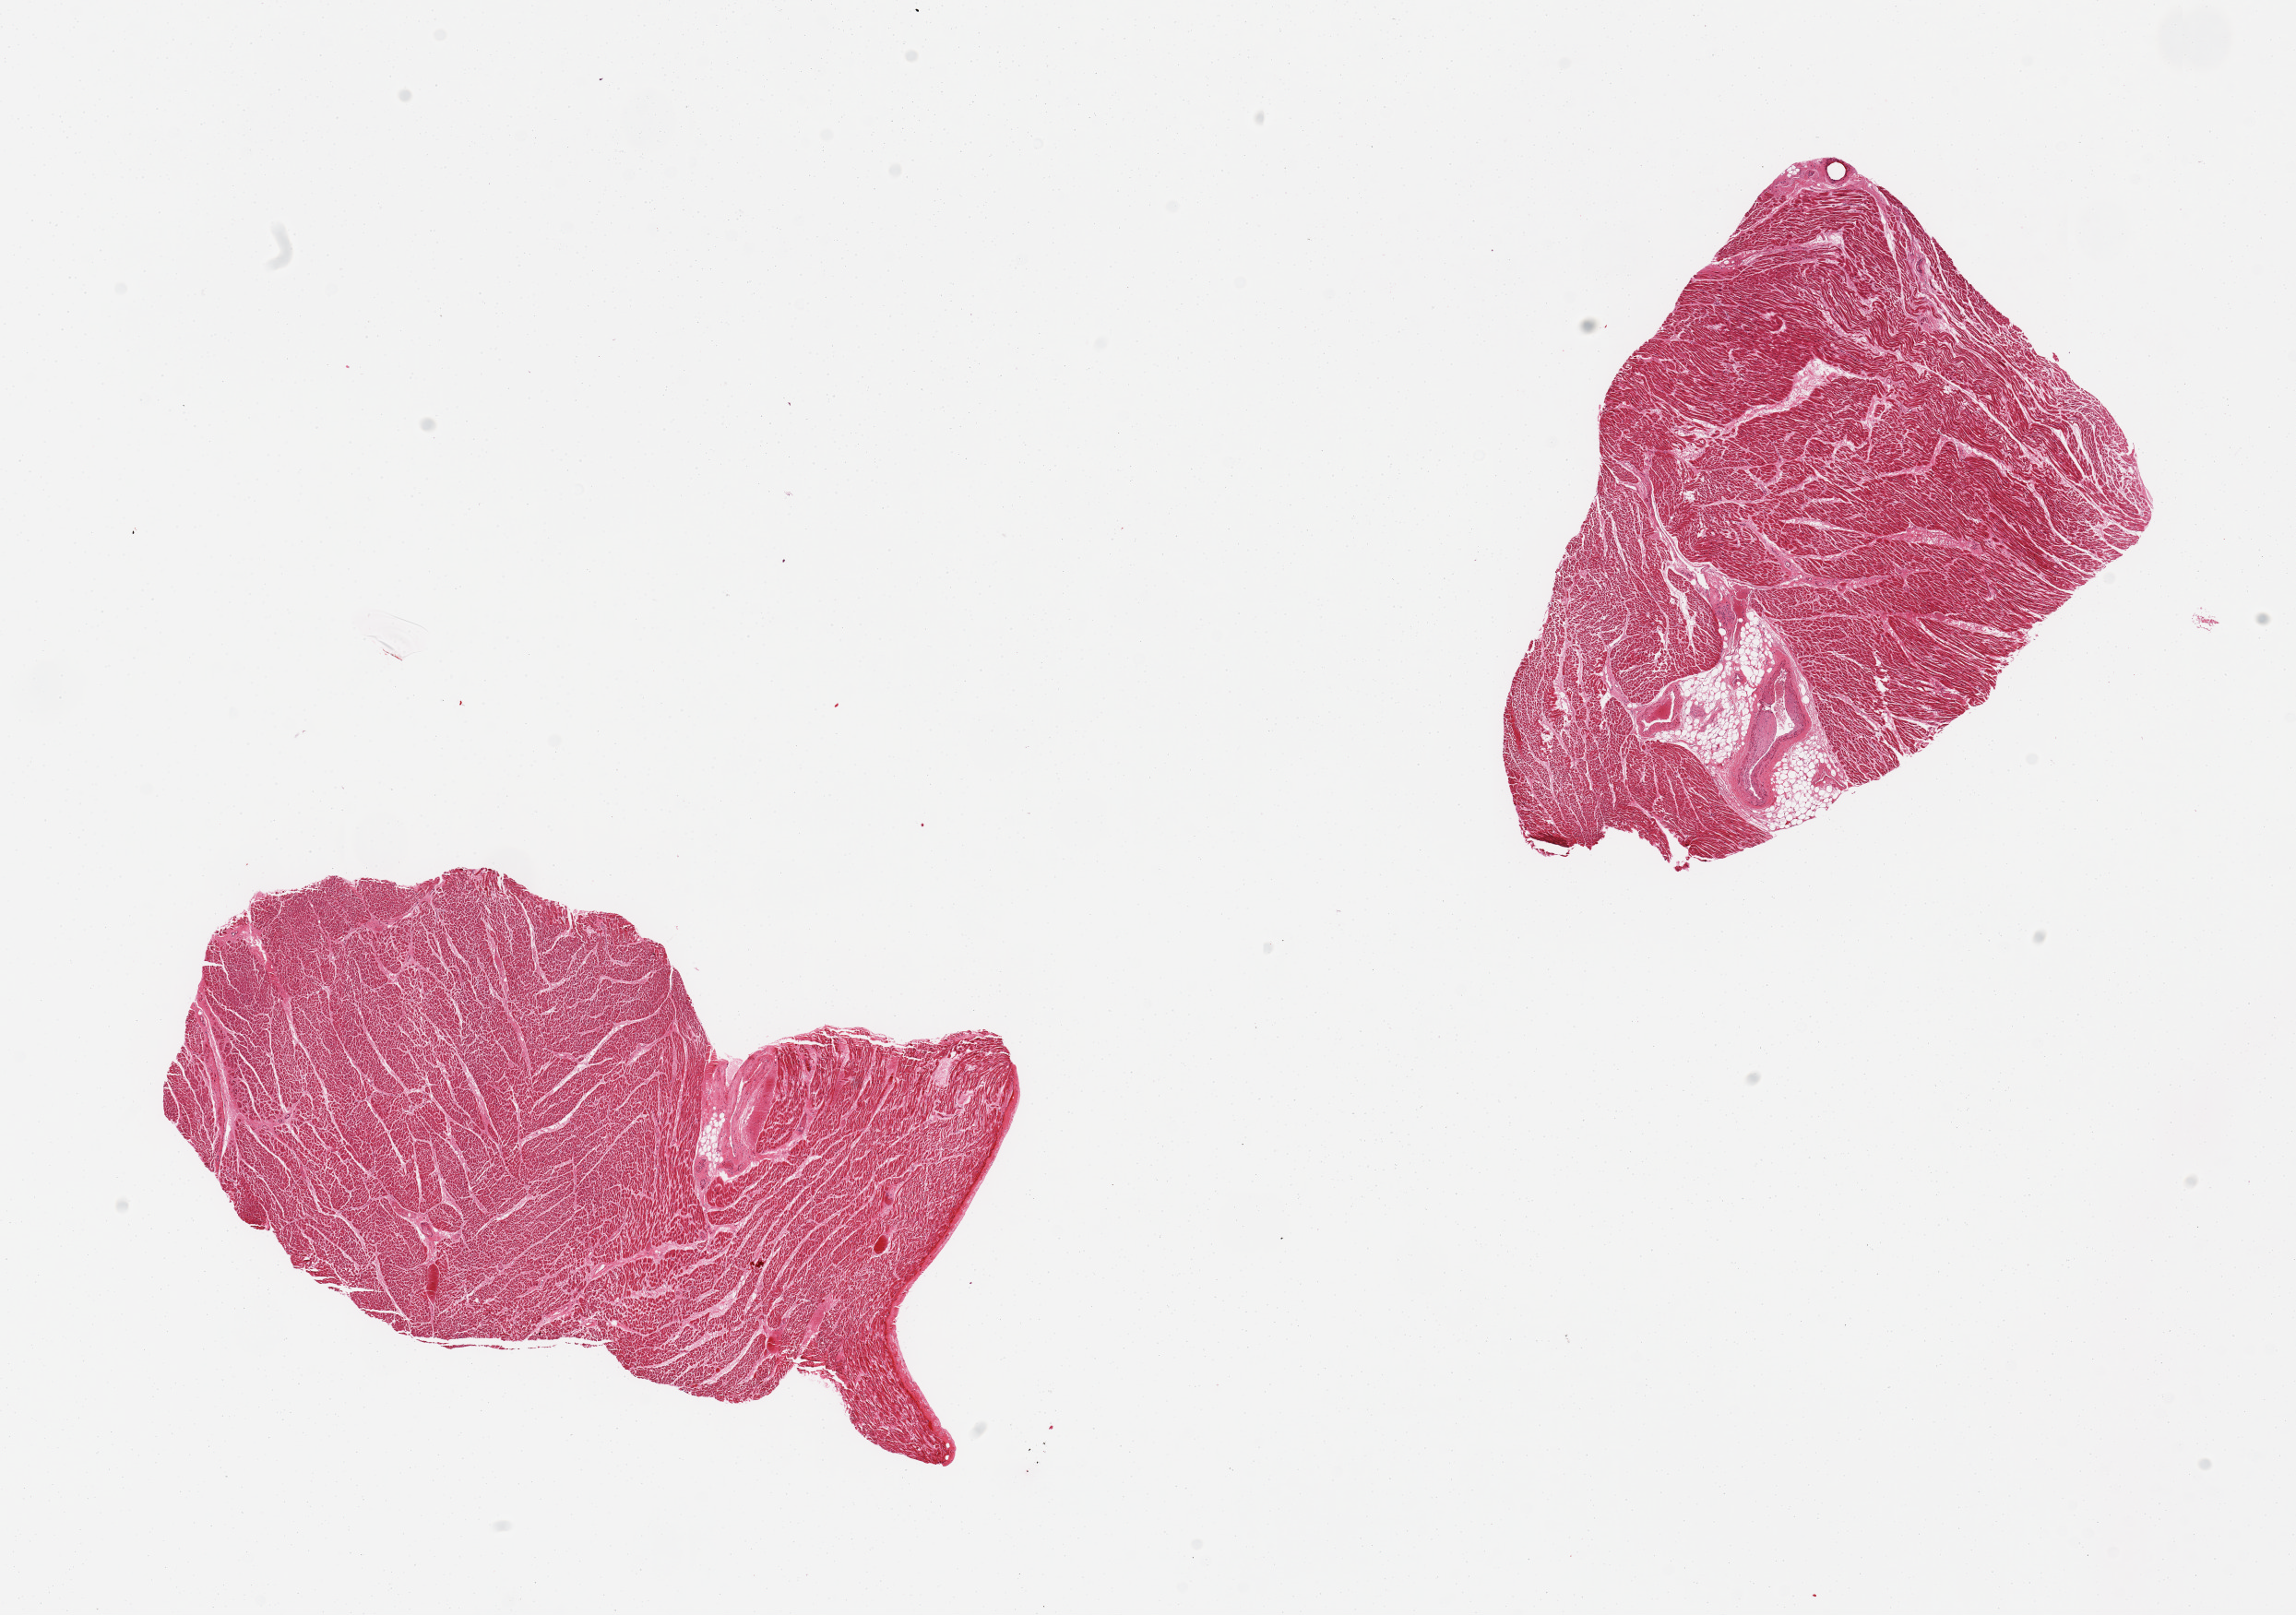
Digitized H&E-stained section, shown as a low-resolution overview of the whole scanned area (about 19.7 x 13.9 mm, from a 20x scan), PAXgene-fixed paraffin-embedded (PFPE) section, target tissue: heart, tissue donor sample.
Reviewer comment on this tissue sample: 2 pieces, few box car nuclei (myocyte hypertrophy), one piece includes ~10% fat/vessels.